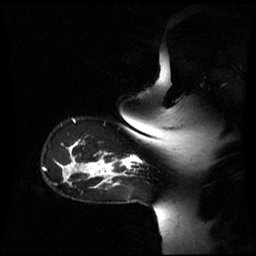
Breast MRI (dynamic contrast-enhanced), one sagittal slice; position 48 of 60 along the scan axis; dynamic contrast-enhanced series, image 2 of 3 at this slice position (ordered by acquisition); 1.5 T; TE 4.2 ms, TR 8.4 ms; 2.6 mm slice thickness; 256 × 256 image matrix, field of view 270 × 270 mm. Female patient, age 39 years. From the clinical record (not read from this slice): setting: breast cancer imaged before/during neoadjuvant chemotherapy; receptor status: triple-negative.
Structures marked on this image (semi-automatically segmented with operator editing):
- analysis volume of interest (the breast-tissue region the enhancement analysis was run in; not a lesion): box from (x=105, y=153) to (x=141, y=179) px
- tumour enhancement mask (voxels above the 70 % enhancement threshold inside the analysis volume of interest): (x=105, y=157)–(x=140, y=179)